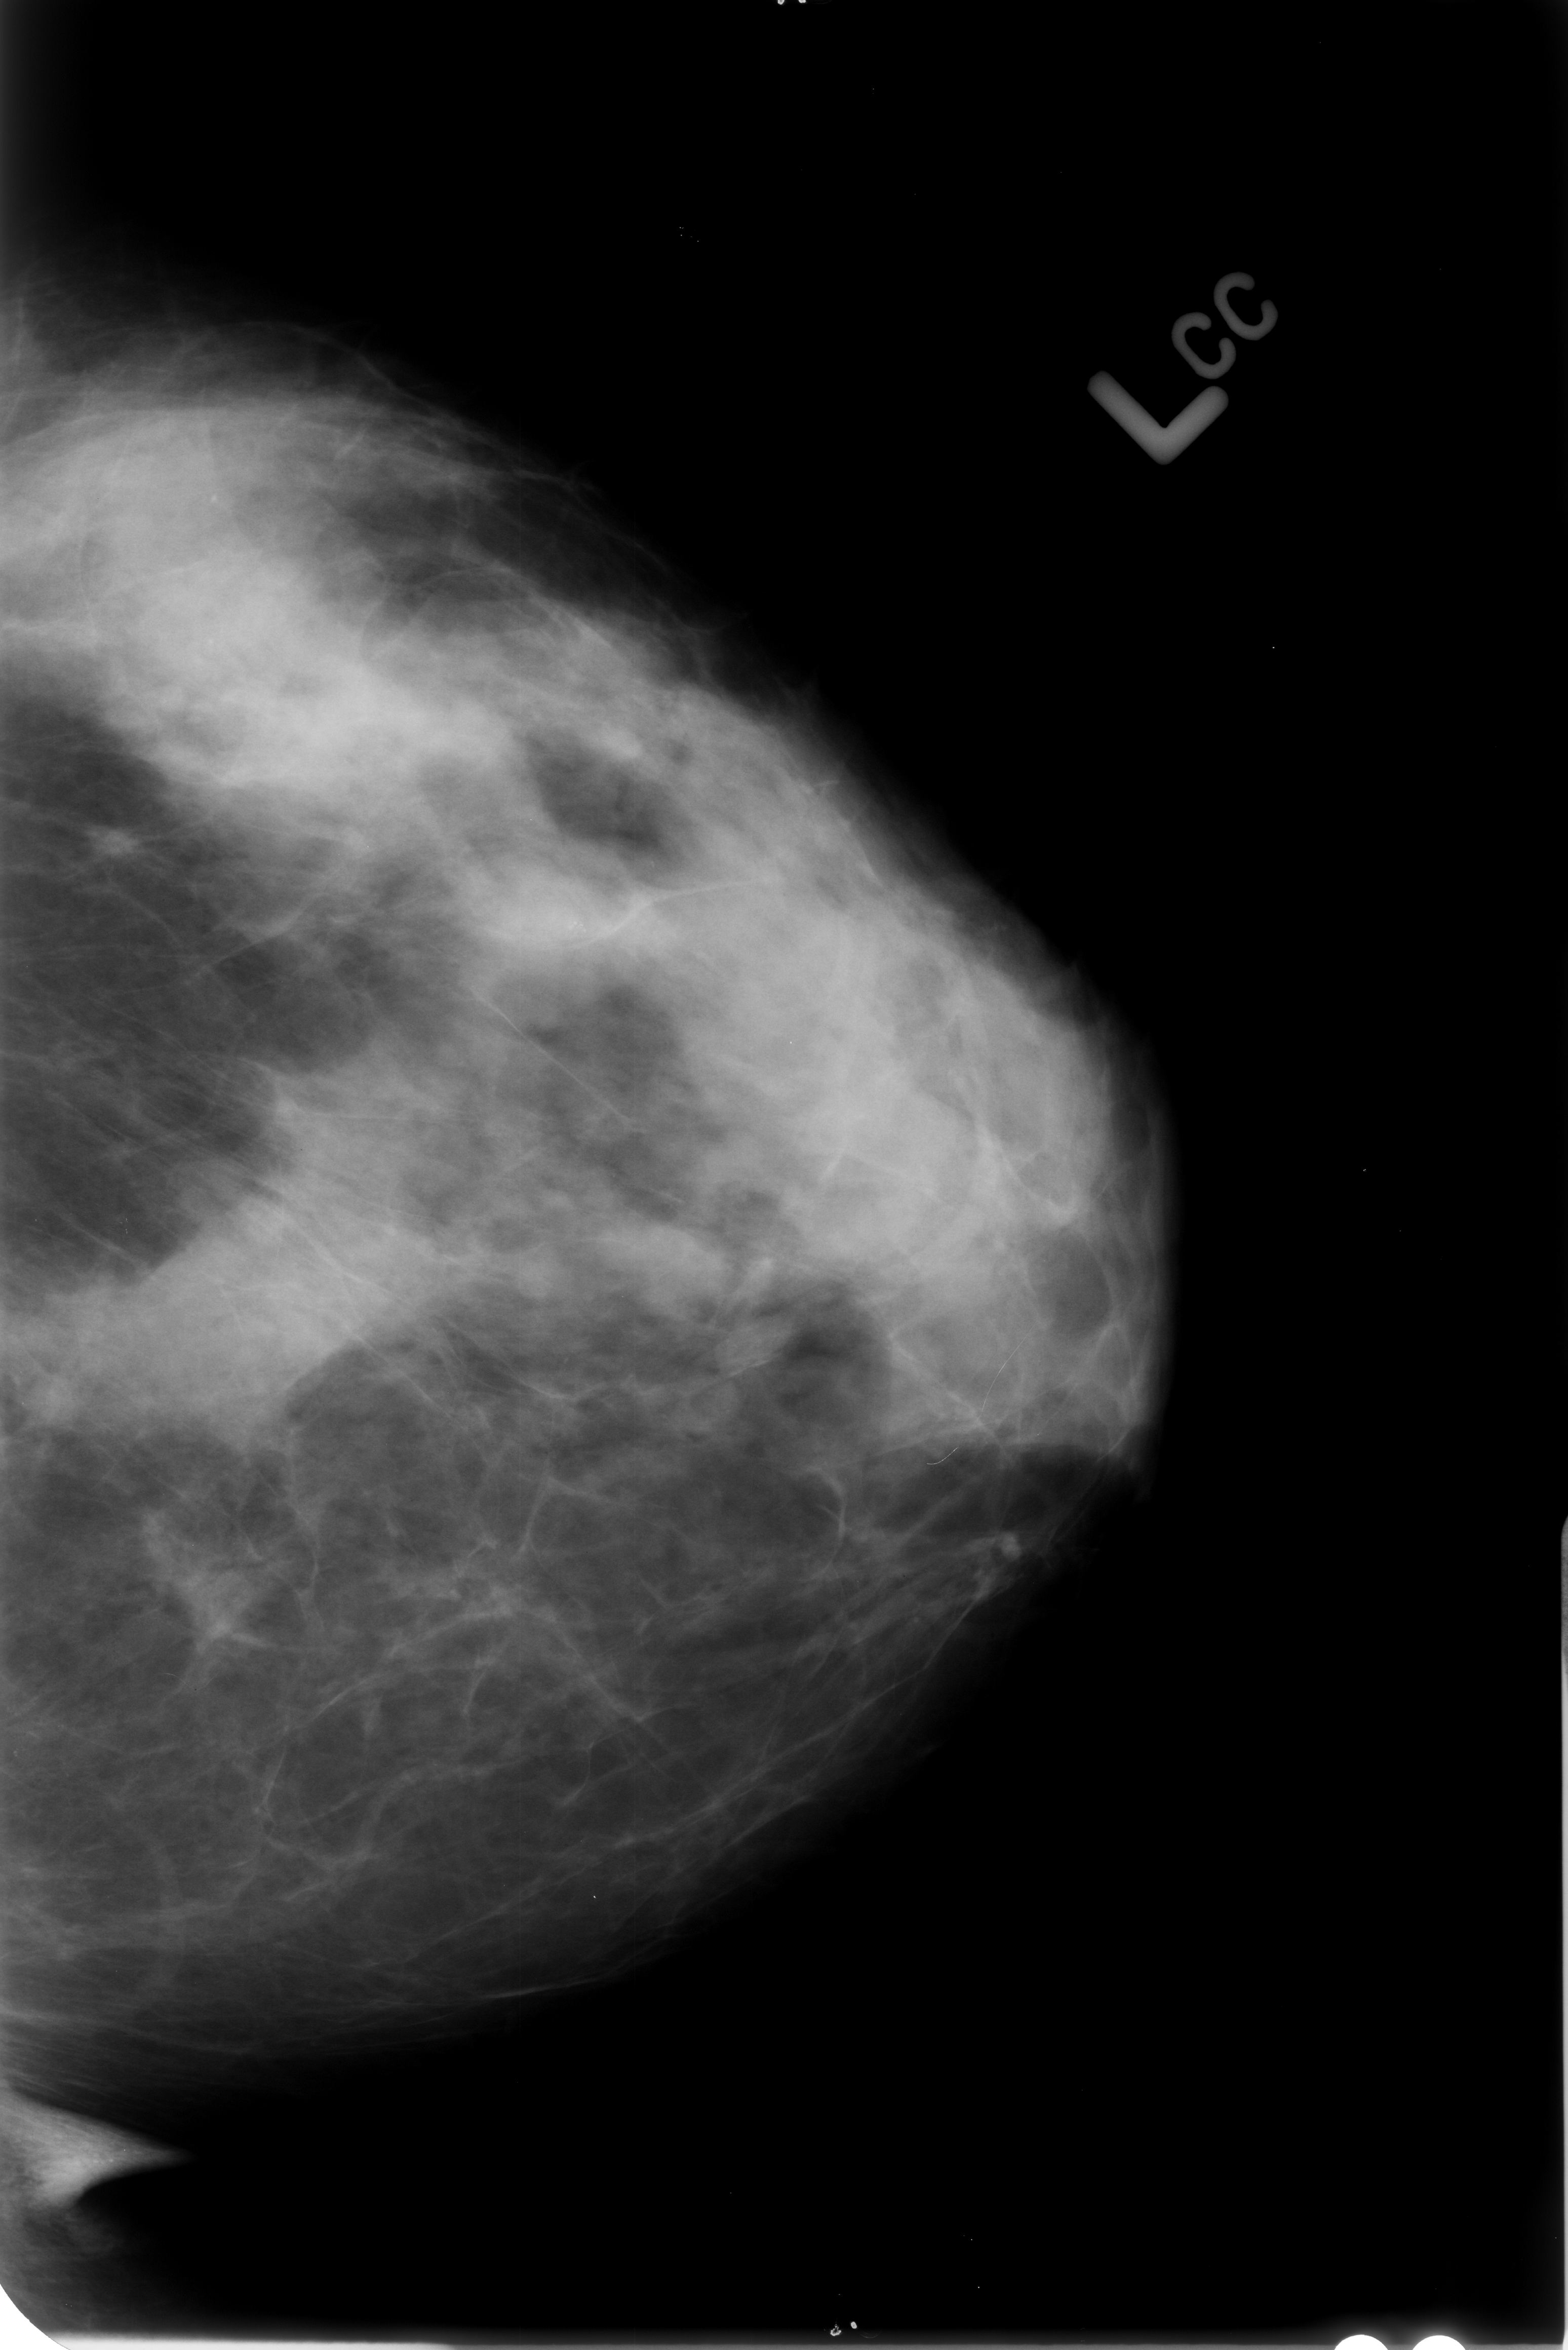
Scanned film-screen mammogram. Left breast. CC view. BI-RADS breast density category 3 (scale 1–4). 1568 × 2350 image matrix.
Marked abnormalities (boxes around the expert regions of interest):
- calcifications, morphology pleomorphic, distribution clustered; BI-RADS assessment category 4; pathology result (as recorded, not read from the image): benign: bounding box <510,858,633,998> (left, top, right, bottom; pixels)